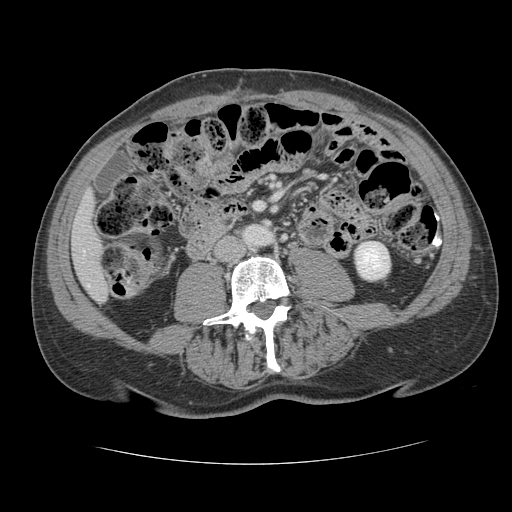
Contrast-enhanced abdominal CT, one axial slice. Position 26 of 134 along the scan axis. 120 kVp. Intravenous contrast given. Soft-tissue window (W 400 / L 40 HU). 2.5 mm slice thickness. 512 × 512 image matrix, field of view 377 × 377 mm. Male patient, age 68 years. From the clinical record (not read from this slice): diagnosis: colorectal cancer liver metastases, imaged before liver resection; multiple liver metastases: yes; largest metastasis: 2.2 cm; chemotherapy before resection: no.
Annotated regions visible in this slice (expert manual segmentation):
- liver: box from (x=73, y=196) to (x=109, y=300) px
- planned liver remnant (the part of the liver to remain after resection): (x=73, y=196)–(x=109, y=301)